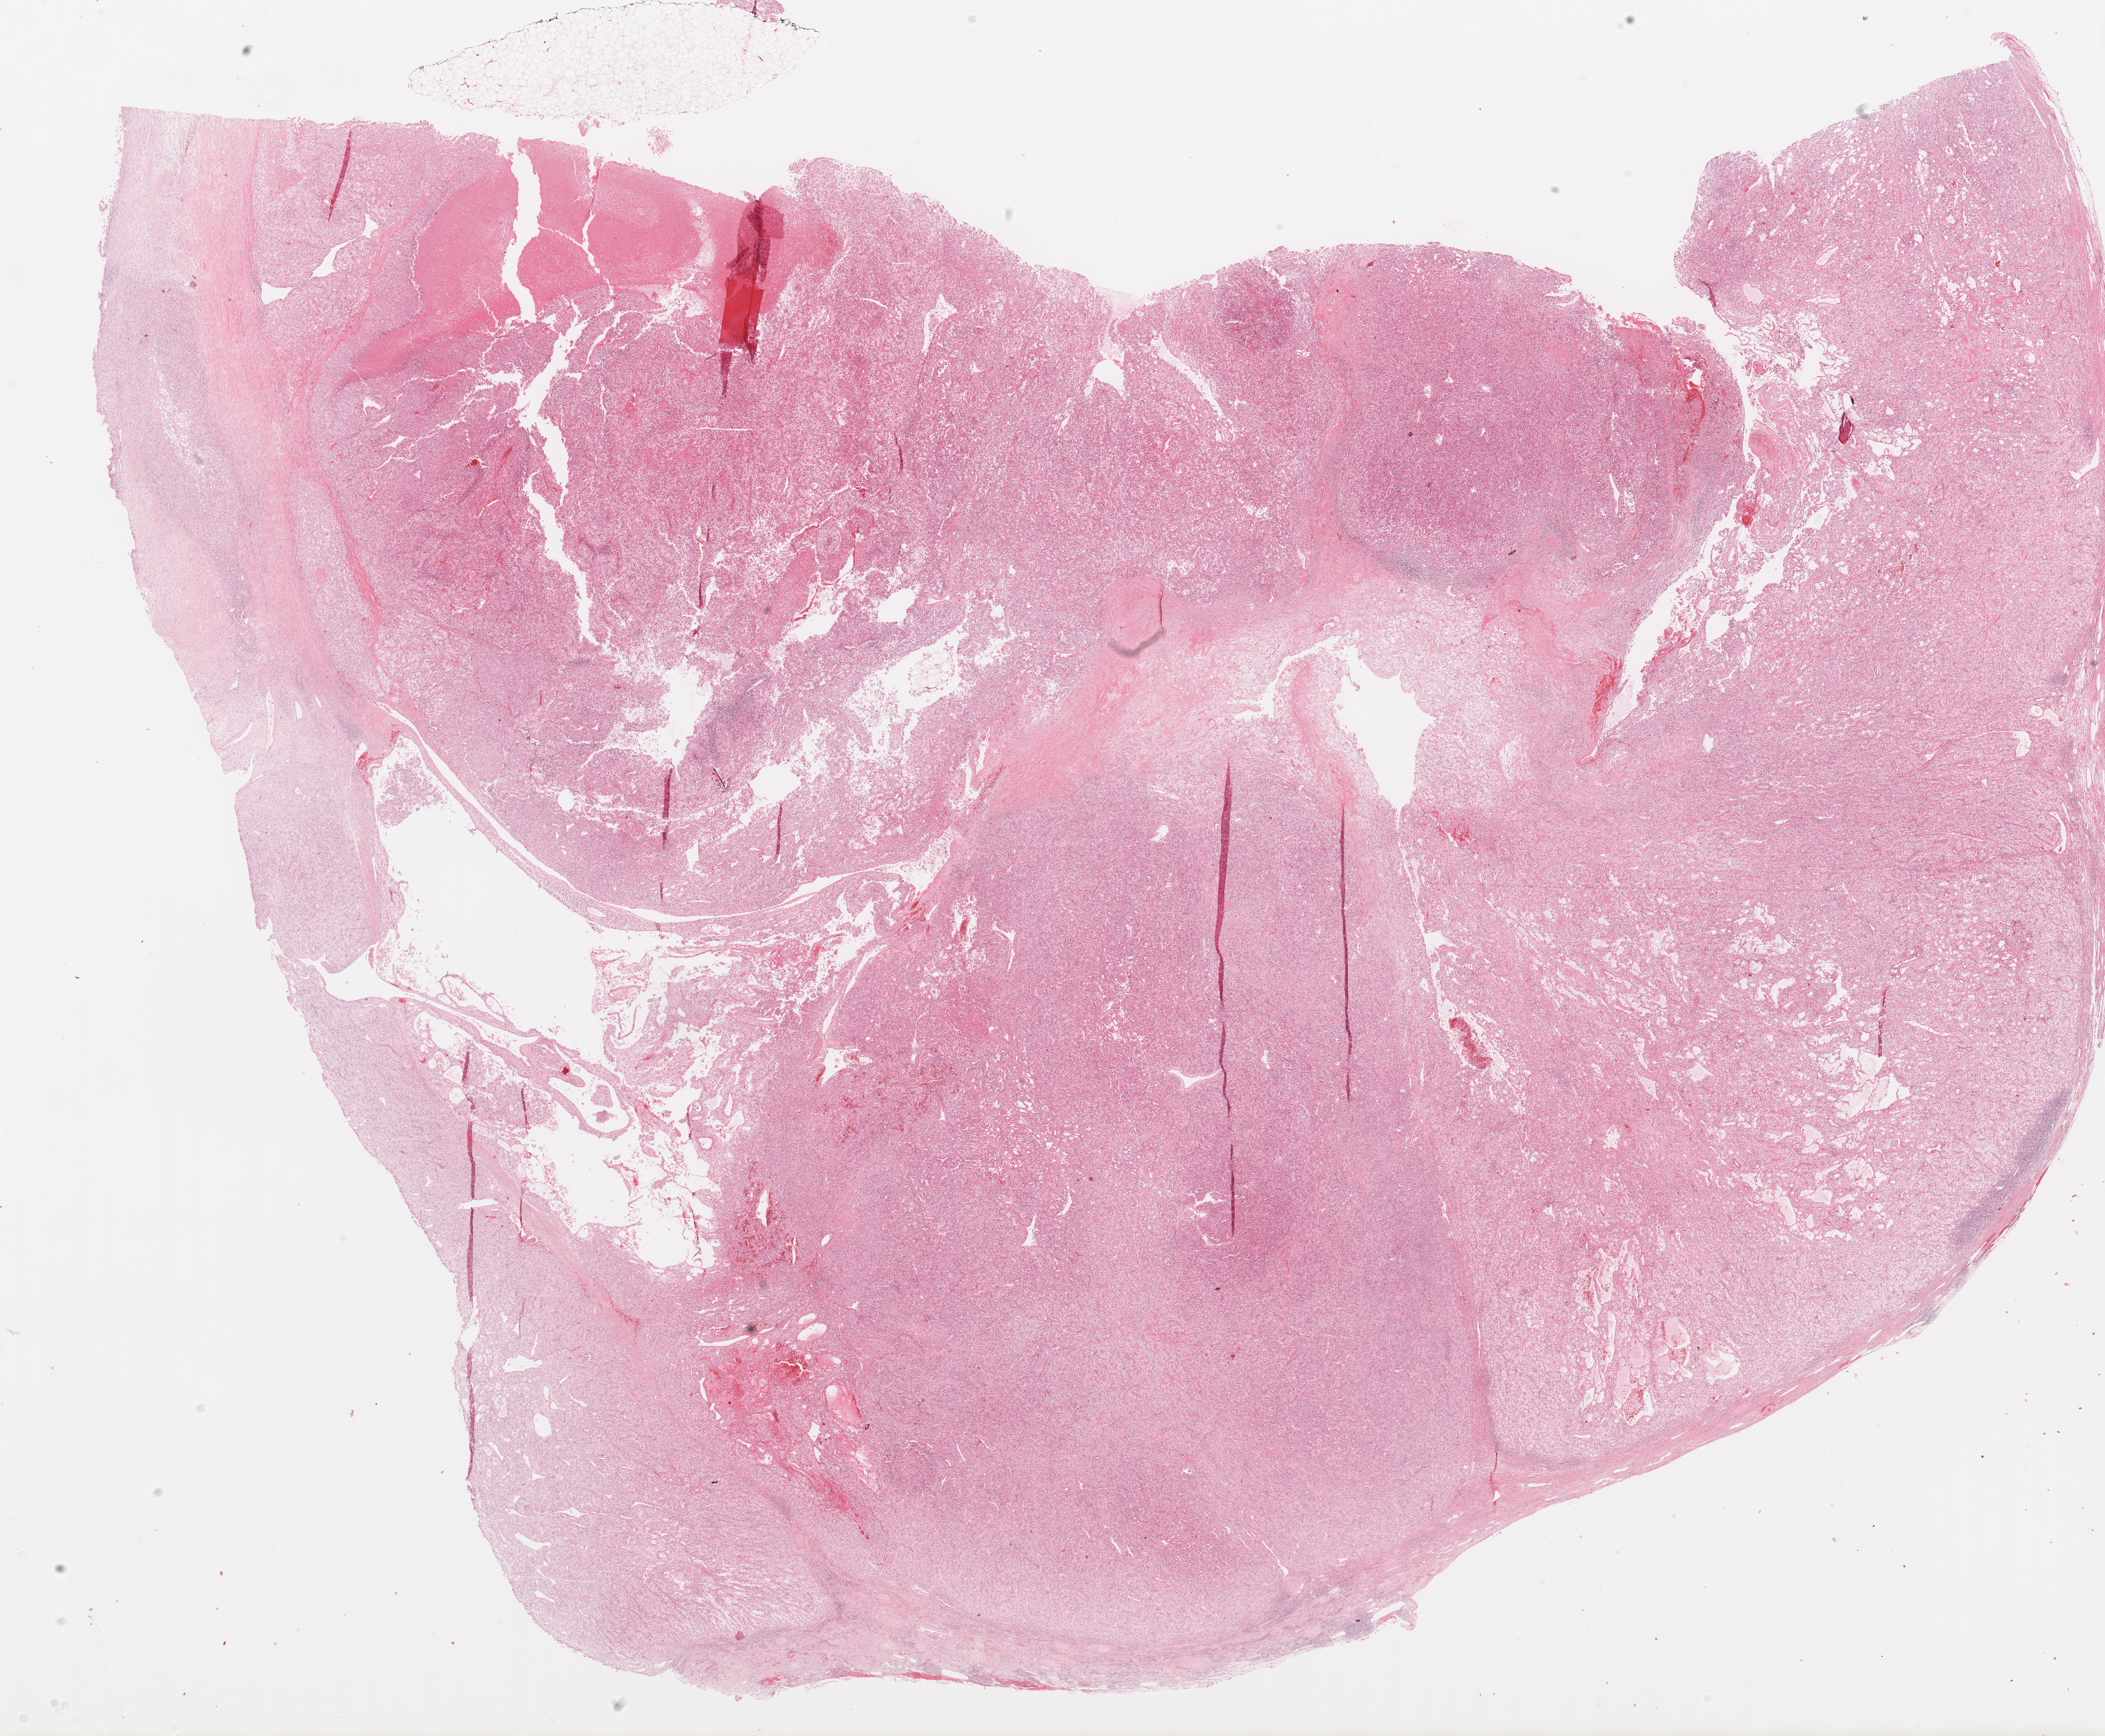
Digitized H&E tissue section (whole slide), a low-resolution overview of the entire scanned area, about 24.1 x 19.9 mm (from a 20x scan); formalin-fixed paraffin-embedded (FFPE) diagnostic section; sample: primary tumour, kidney. Patient: male, age at initial diagnosis 68 years. Histologic grade: G2 (moderately differentiated).
Lymph nodes positive (case pathology): 0 of 2 examined. Pathologic diagnosis: Clear cell adenocarcinoma, NOS. AJCC pathologic stage: I. Laterality: right.